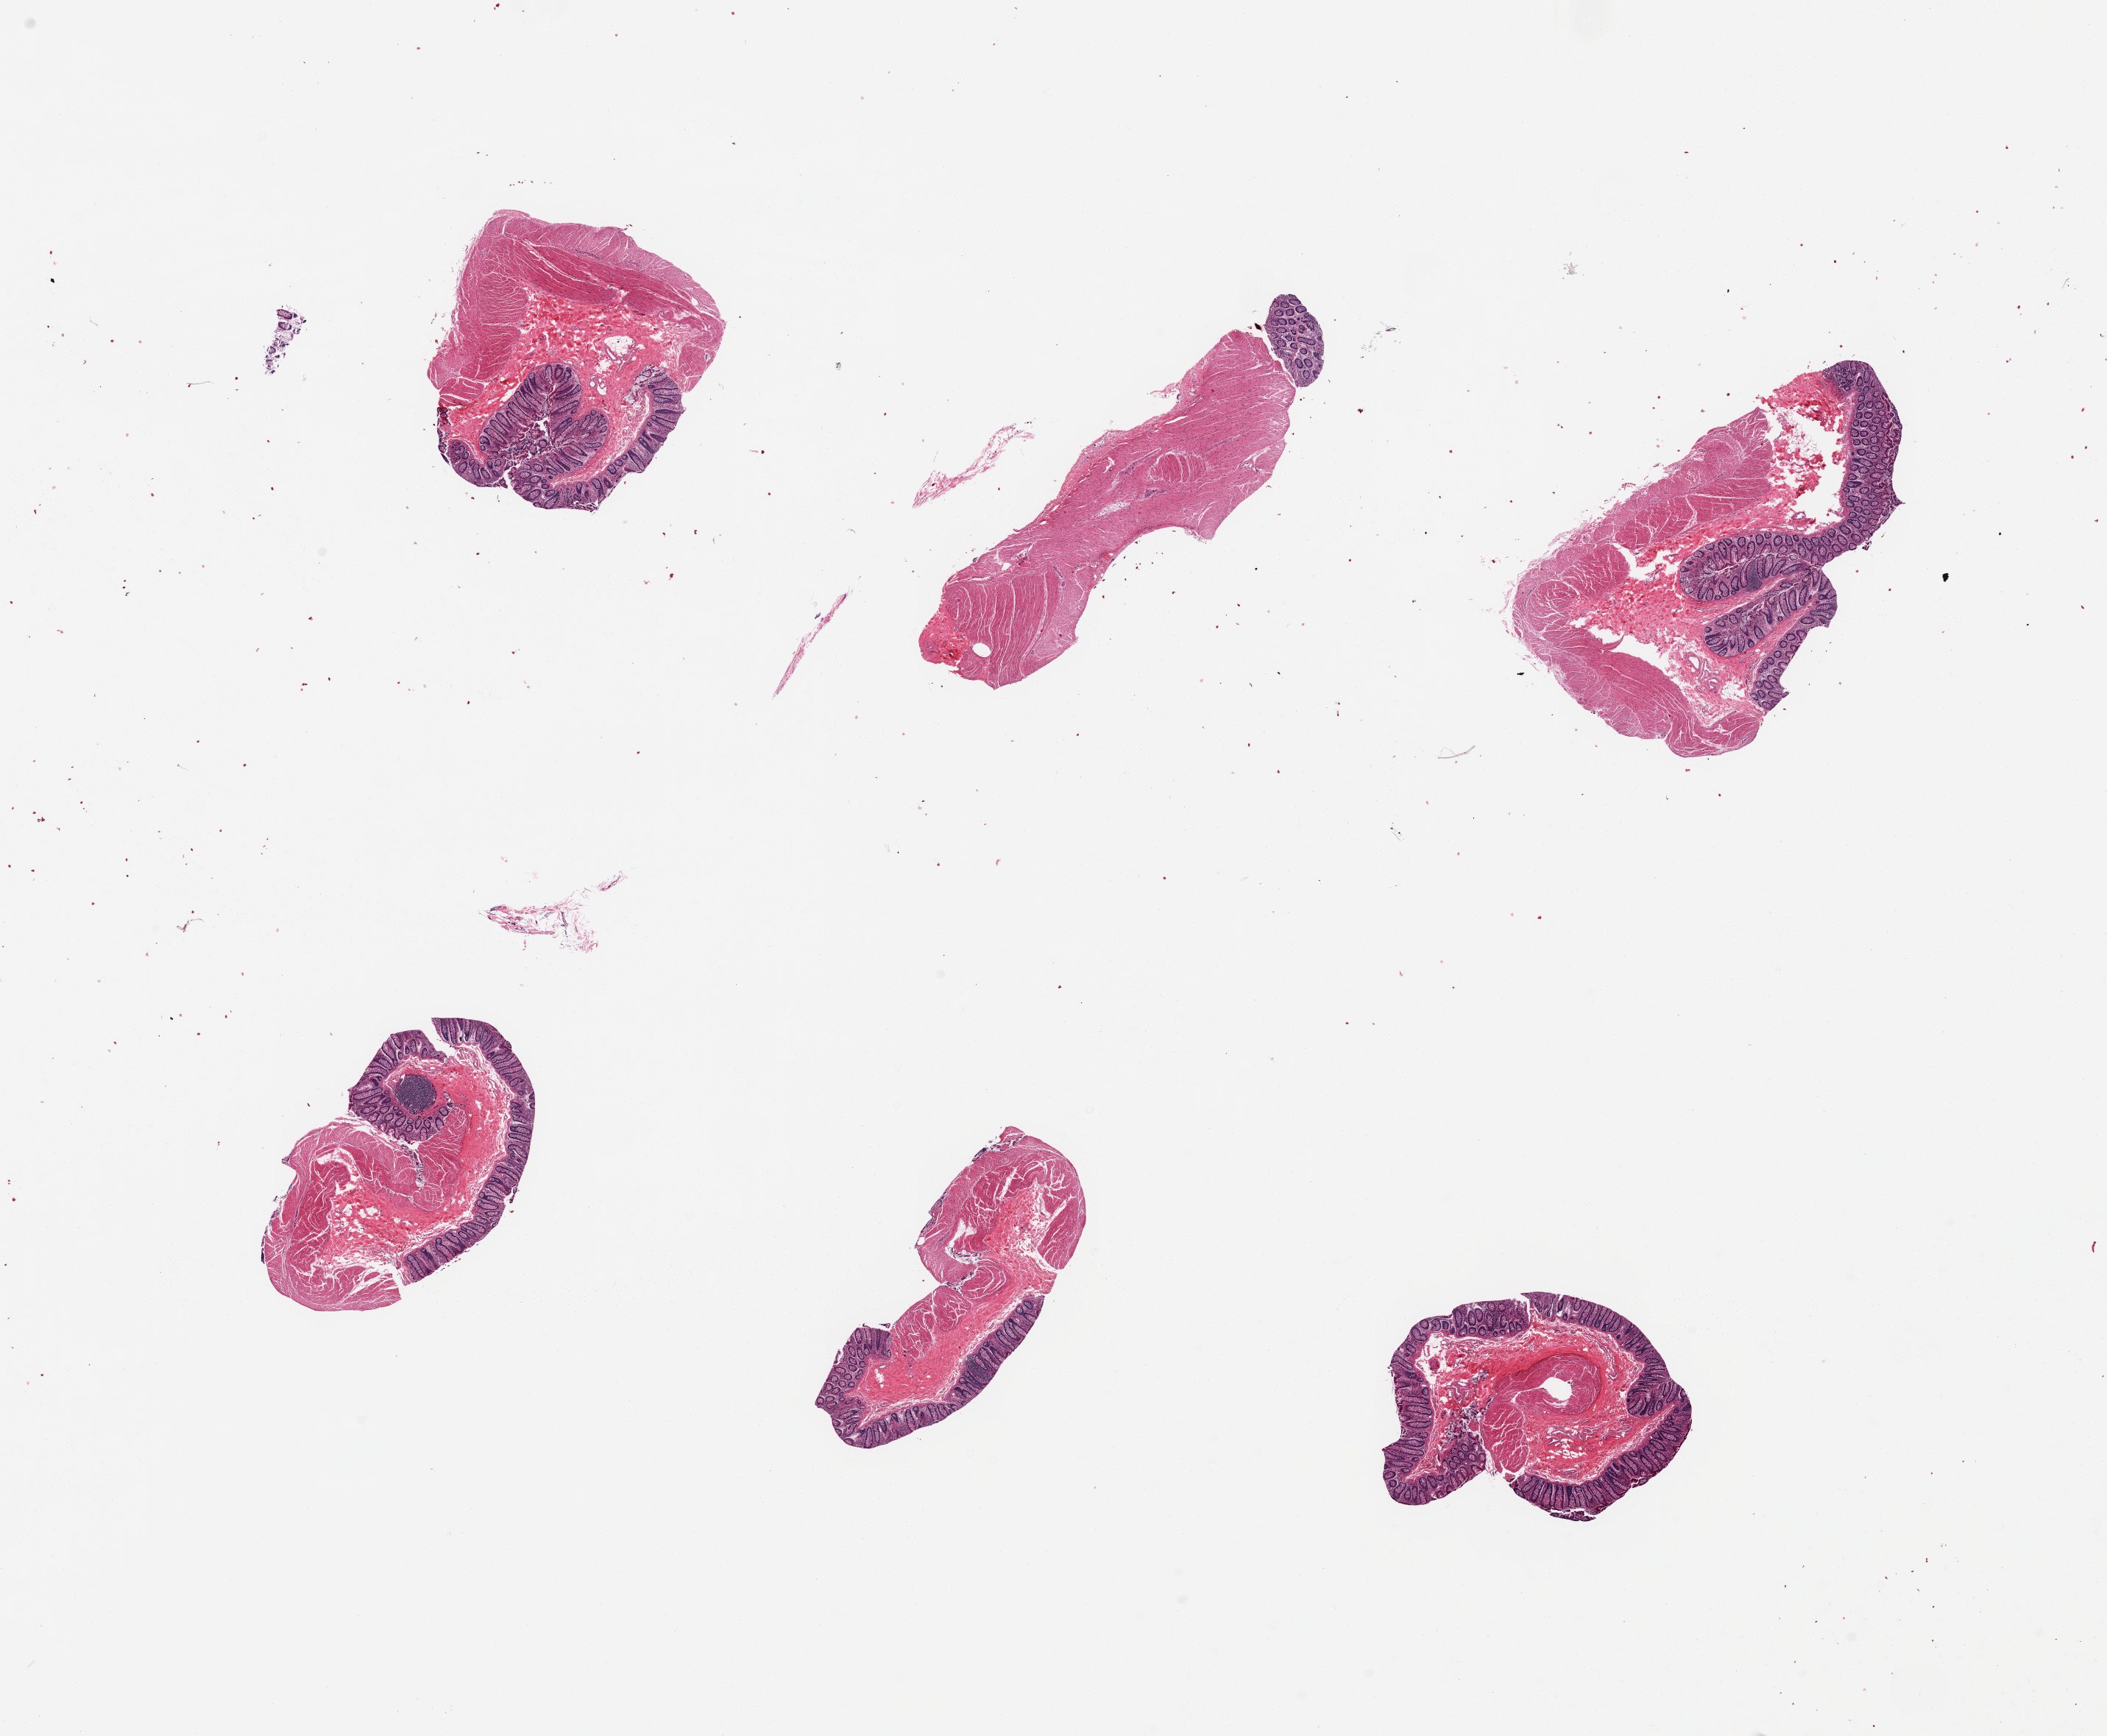
Digitized H&E-stained section, shown as a low-resolution overview of the whole scanned area (about 22.6 x 18.7 mm, from a 20x scan); PAXgene-fixed, paraffin-embedded tissue; sampled site (target tissue): transverse colon; tissue donor sample. Donor: male.
- review note (as recorded): 6 pieces; target mucosa and muscularis present